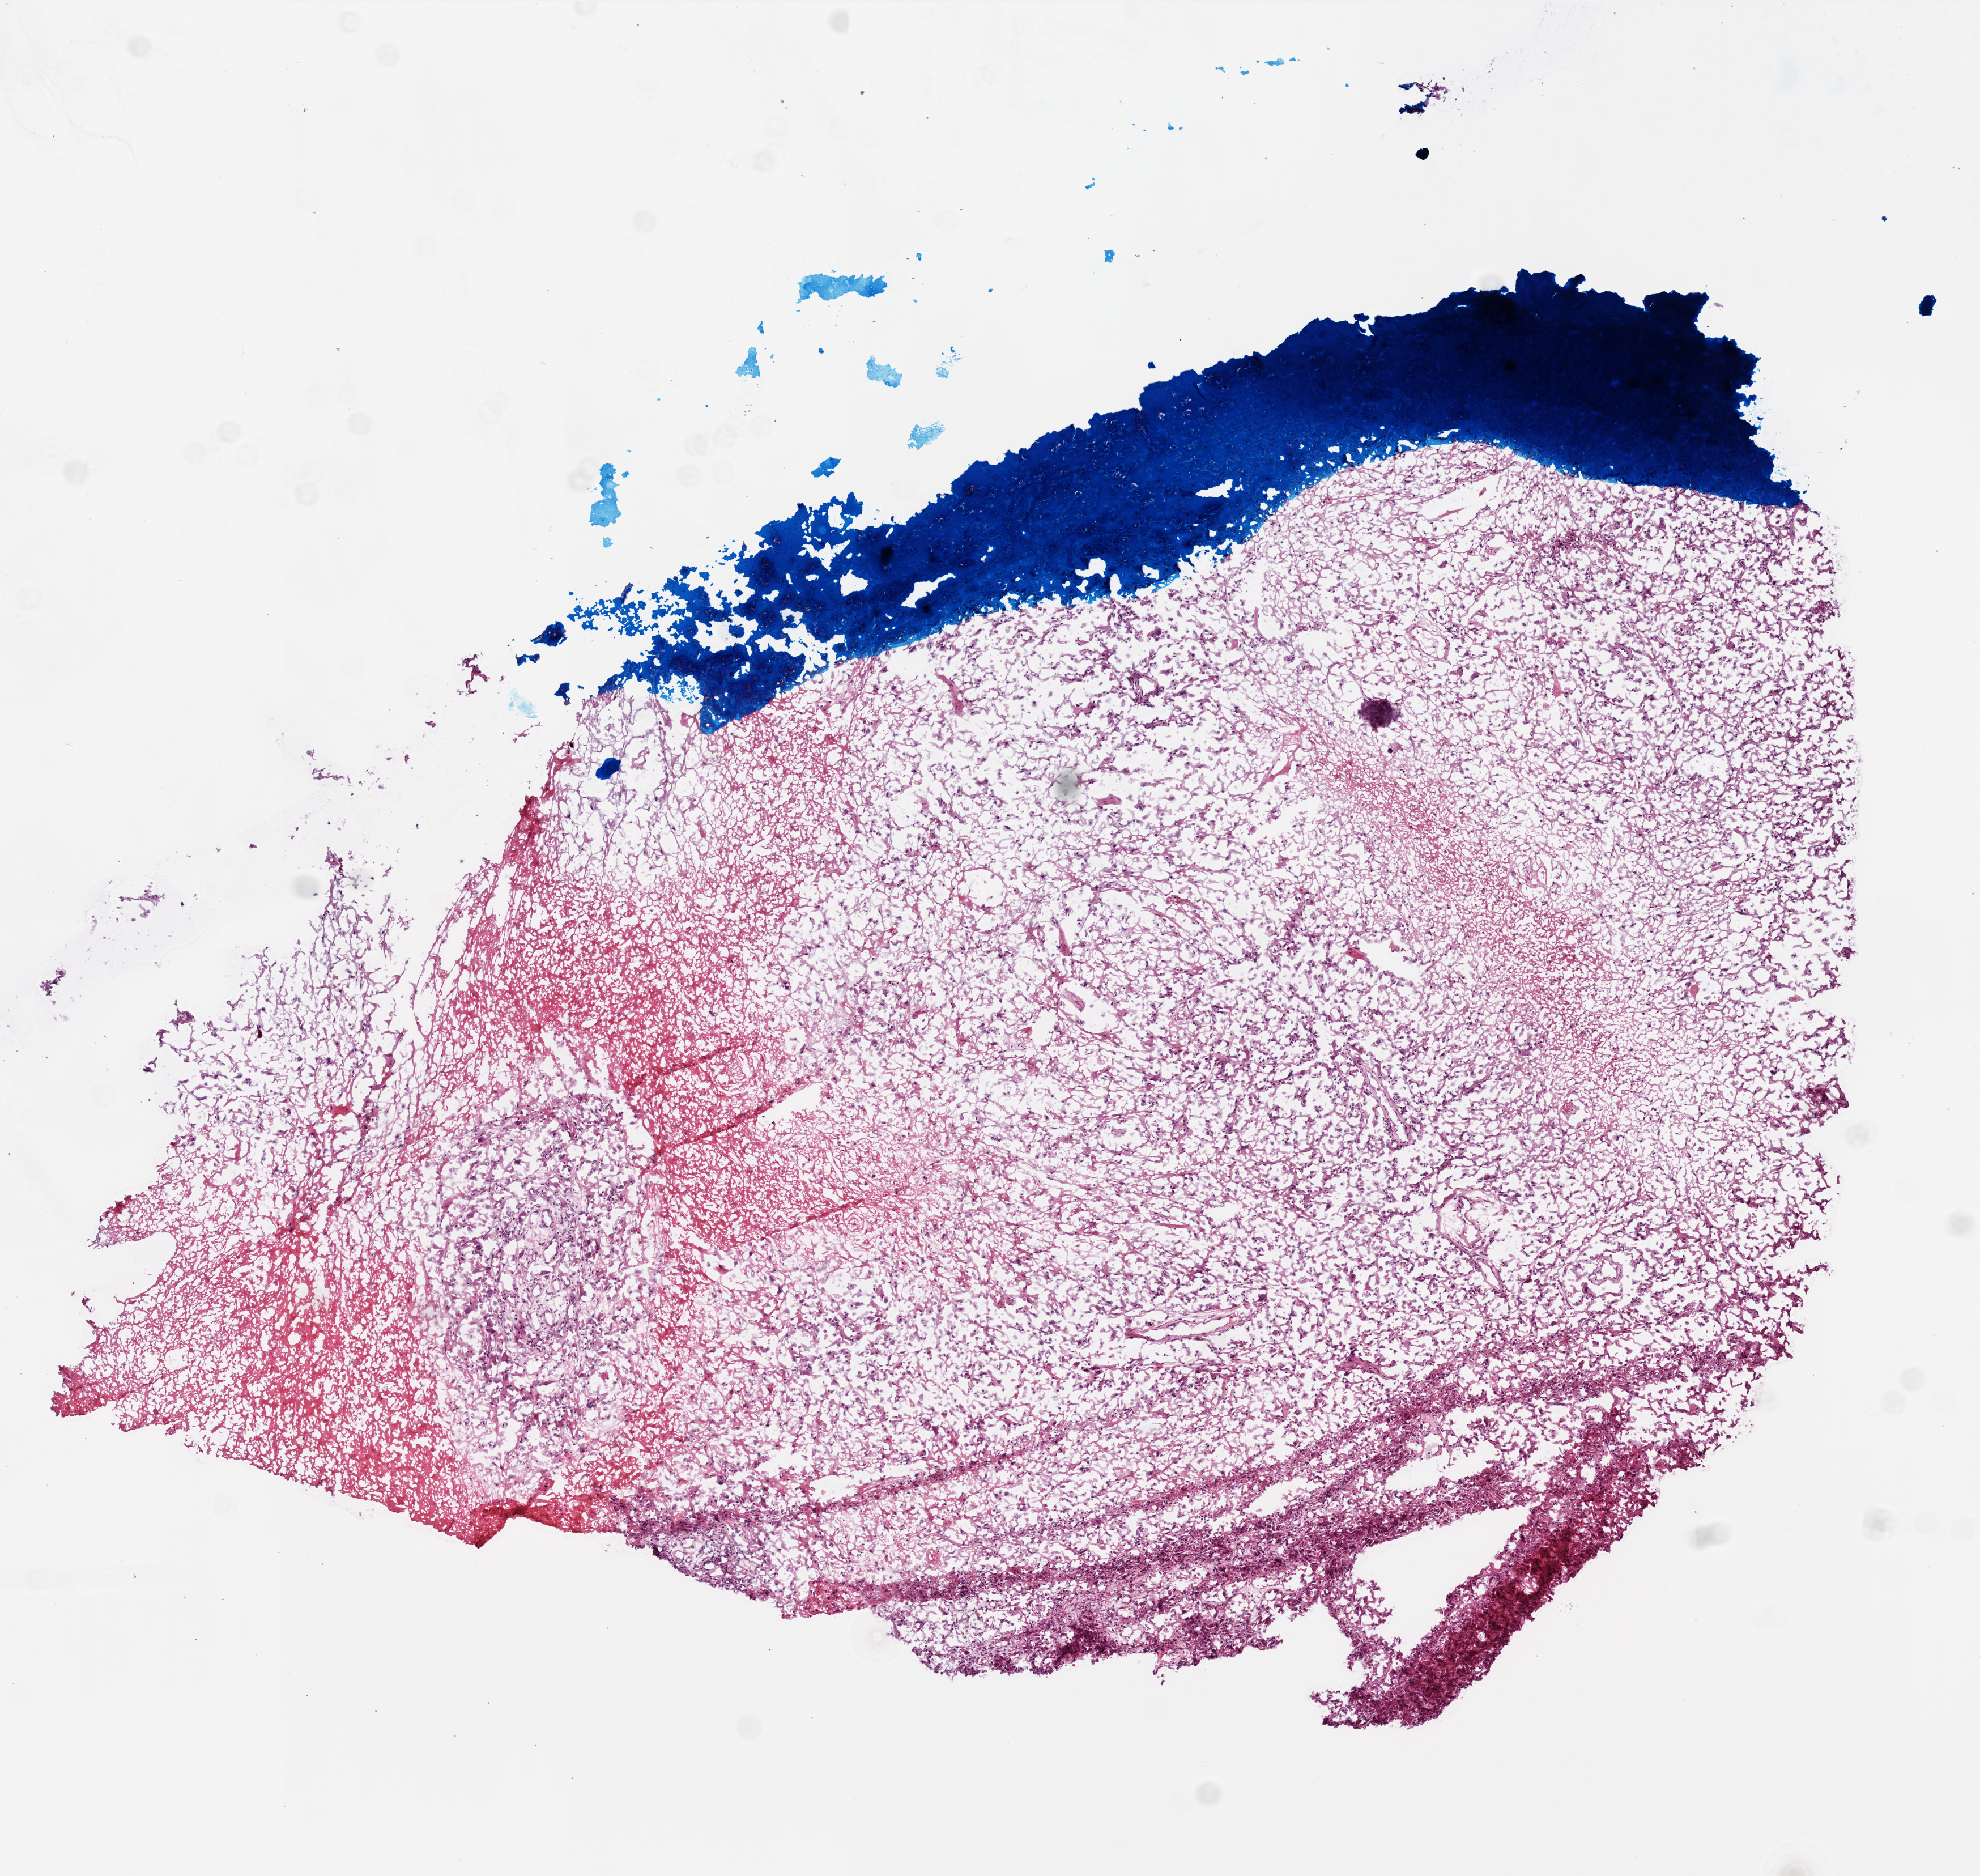
H&E whole-slide image — shown as a low-resolution overview of the whole scanned area (about 7.0 x 6.6 mm), frozen section from the top of the tissue portion, brain, primary tumour sample. Patient: male, age at initial diagnosis 48 years. Pathologist review of this section (percent, as recorded): tumour cells 75%, tumour nuclei 100%, normal cells 0%, stromal cells 0%, necrosis 25%.
- diagnosis: Glioblastoma